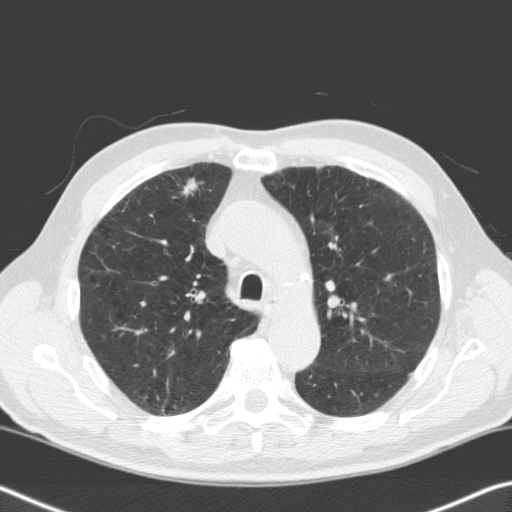
Low-dose screening chest CT, one axial slice. Position 124 of 170 along the scan axis. Lung window (W 1500 / L -600 HU). 512 × 512 image matrix.
Structures marked on this image (outlined manually by an expert reader):
- lesion 1 (tumor, upper lobe of right lung): bounding box [x1, y1, x2, y2] px = [183, 178, 198, 196]